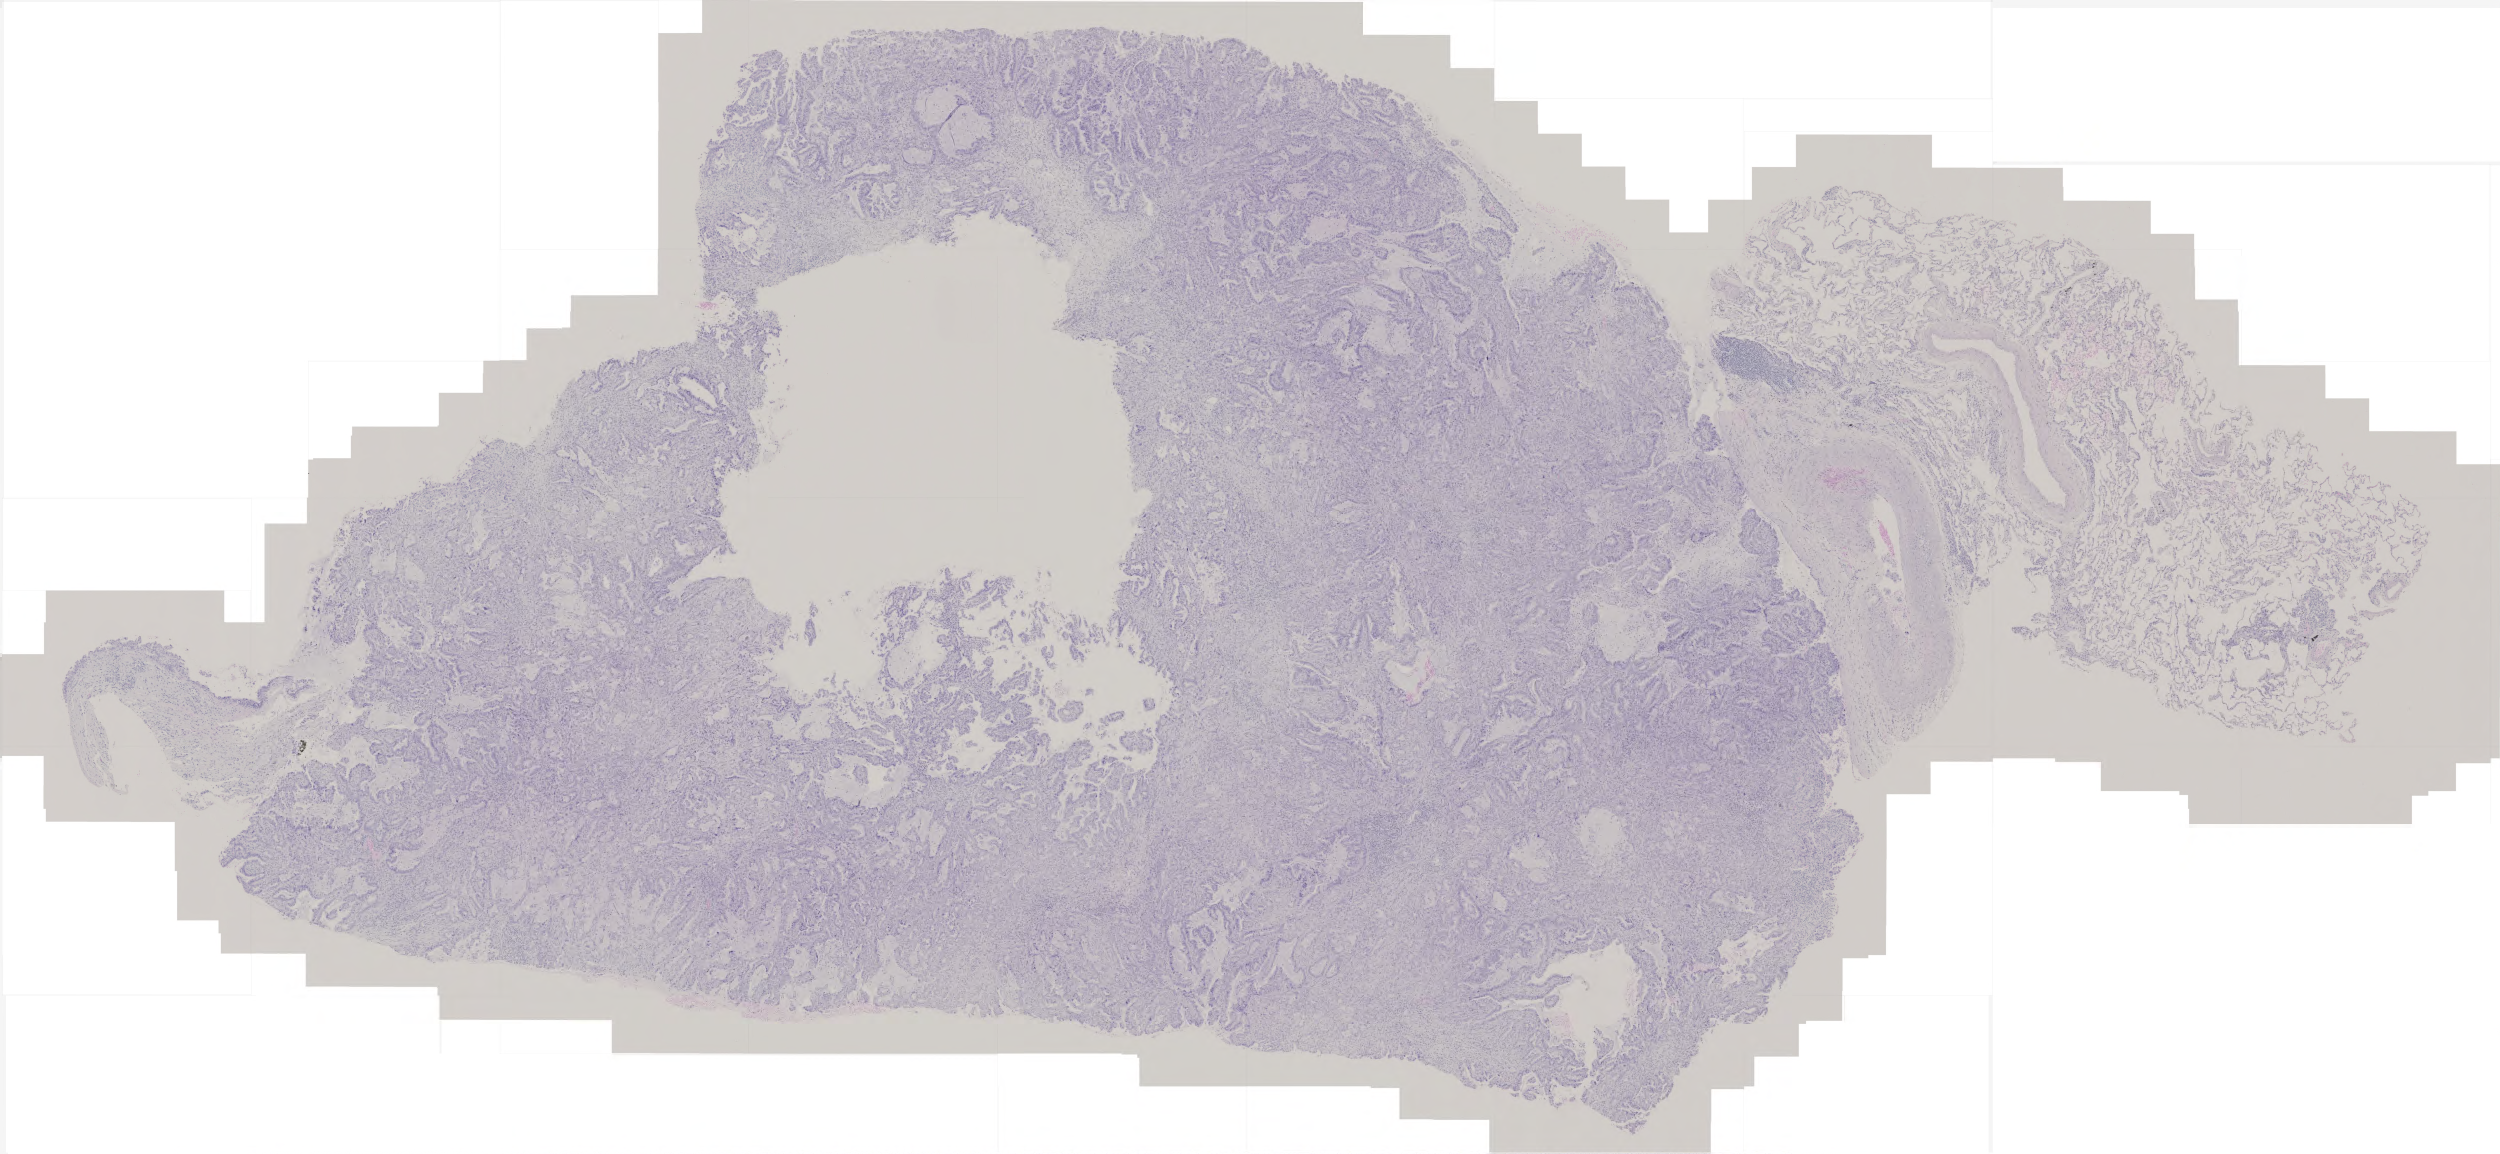
H&E-stained whole-slide image, shown as a low-resolution overview of the whole scanned area (about 5.0 x 2.3 mm). Formalin-fixed paraffin-embedded (FFPE) diagnostic section. Lung, primary tumour sample. Female, age 70 years at initial diagnosis.
- laterality: right
- histologic diagnosis: Adenocarcinoma with mixed subtypes (middle lobe, lung)
- AJCC pathologic stage: IV (6th edition)